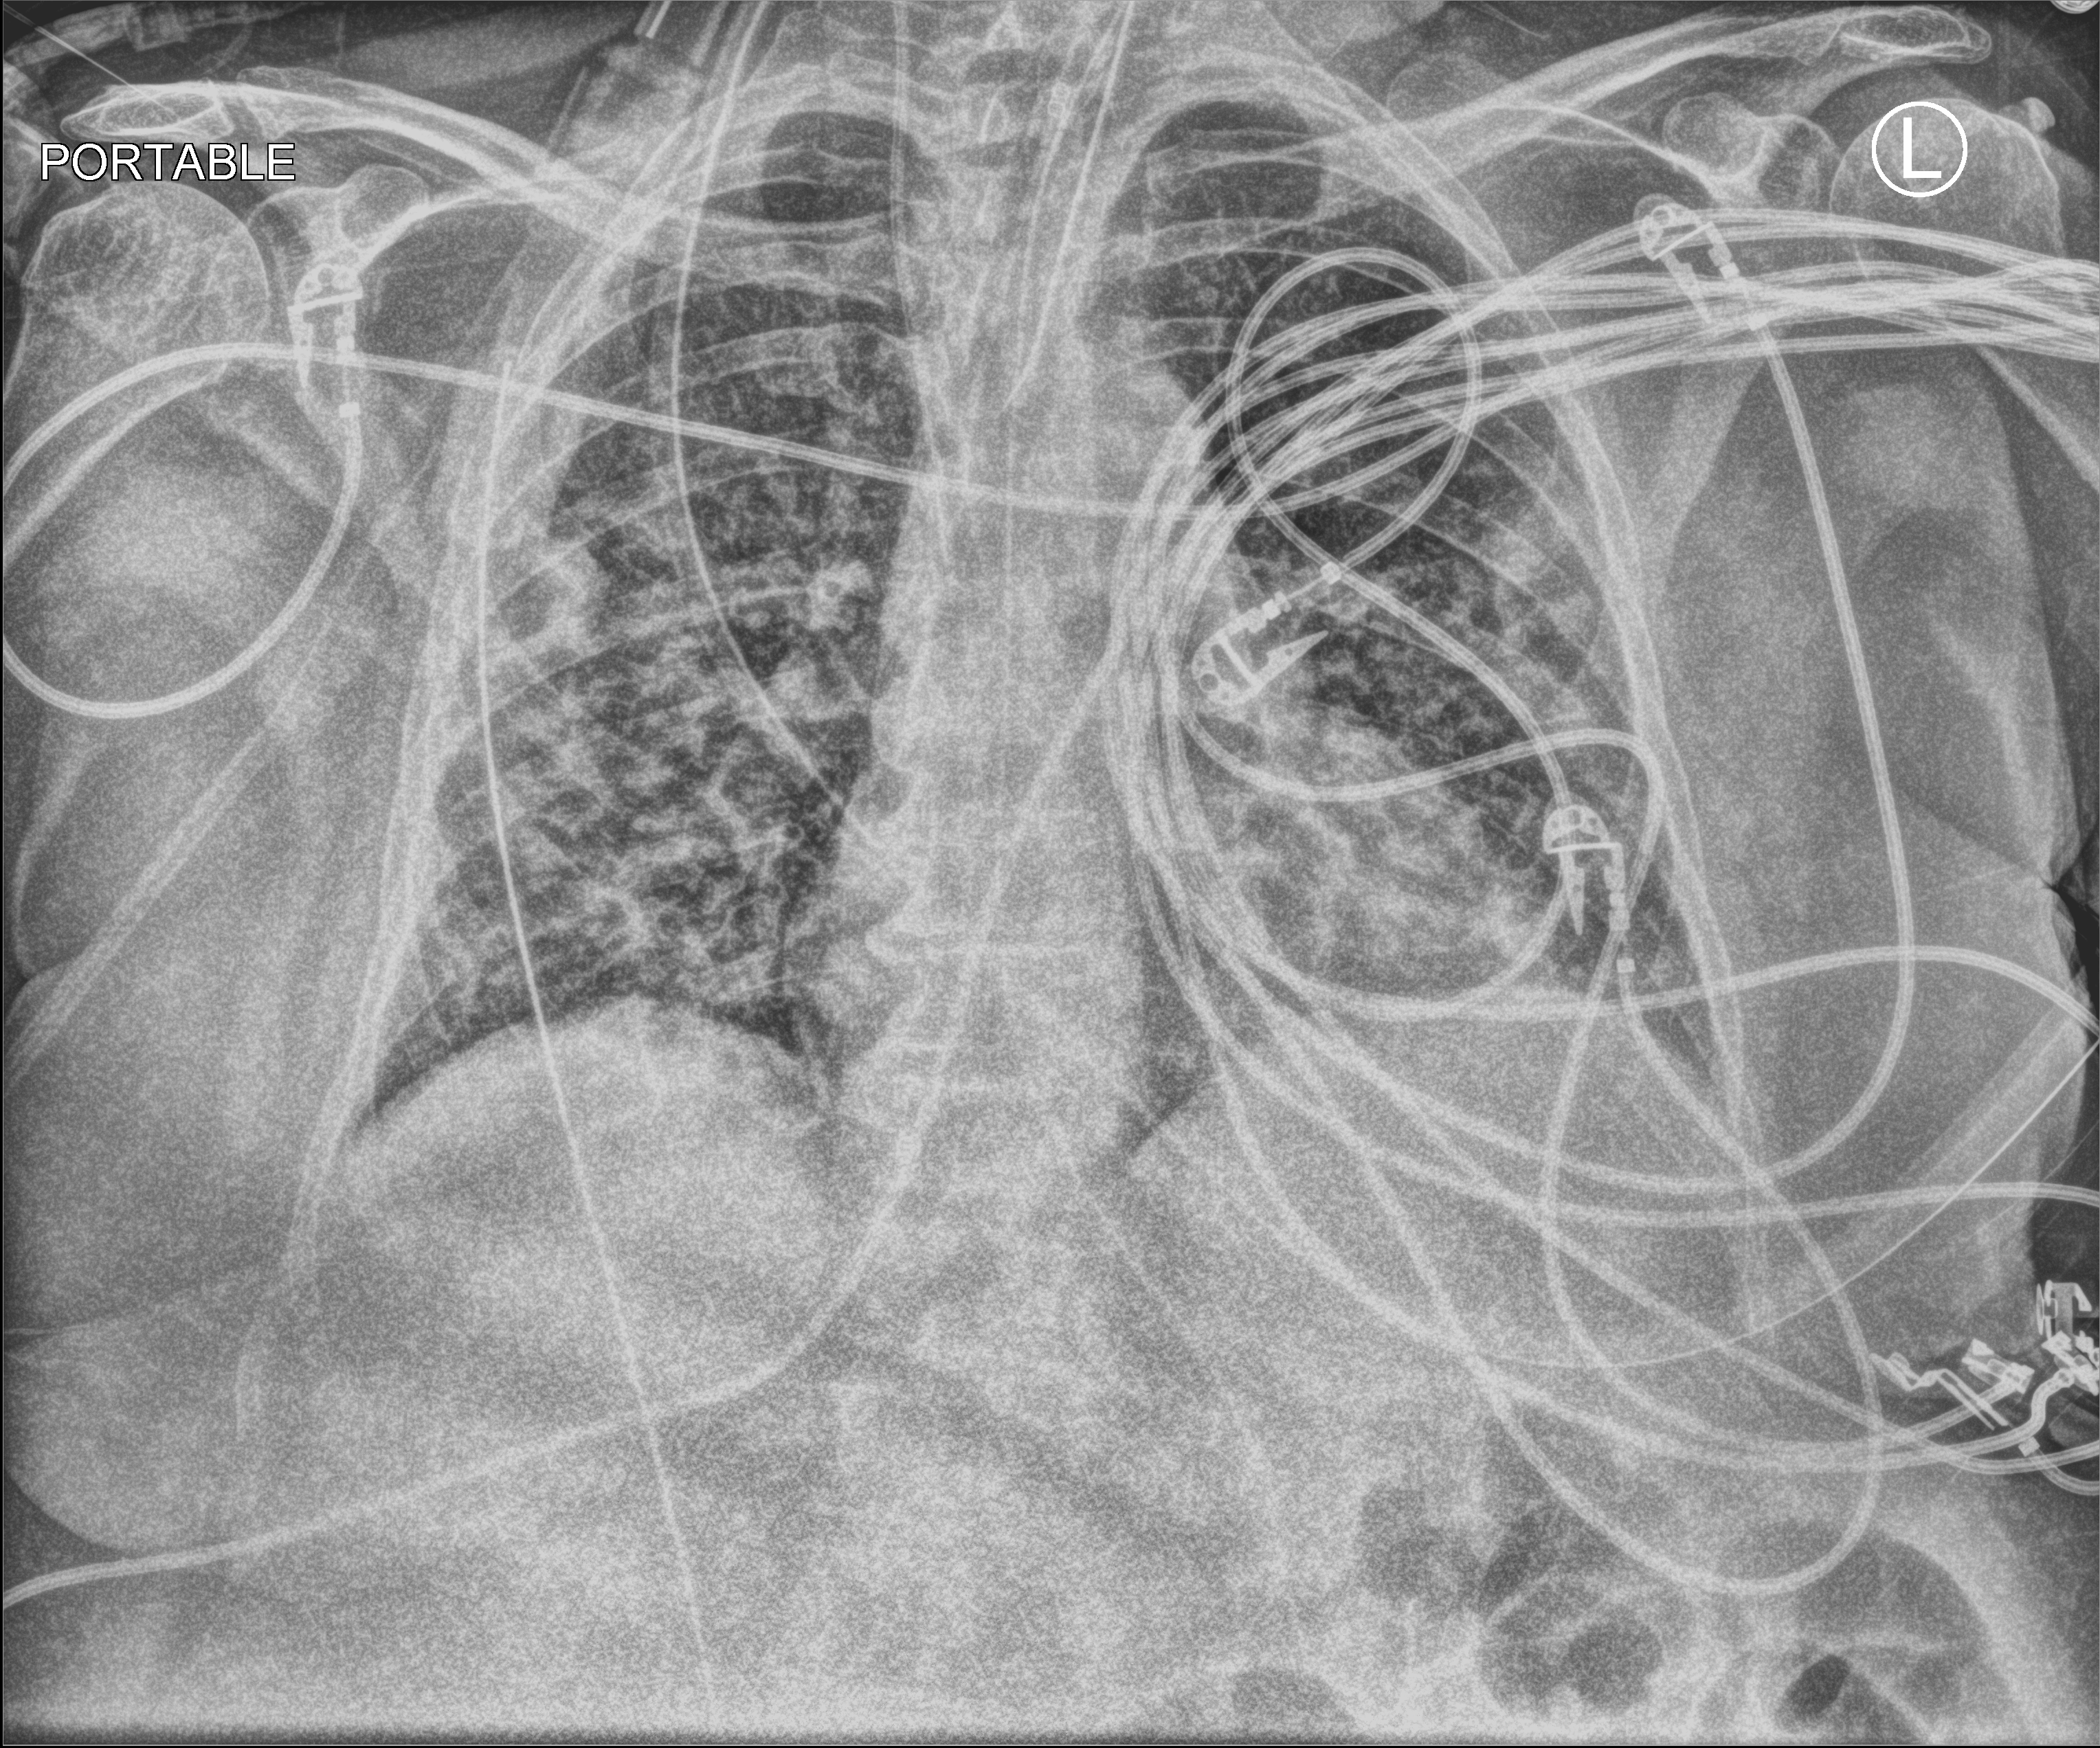
Chest X-ray (portable), anteroposterior (AP) projection. Female patient hospitalised with COVID-19, age 75–90 years.
From the hospital-stay record, not from the radiograph (when in the stay this image was taken is not recorded): admitted to intensive care during this hospital stay: yes; mechanically ventilated during this hospital stay: yes.